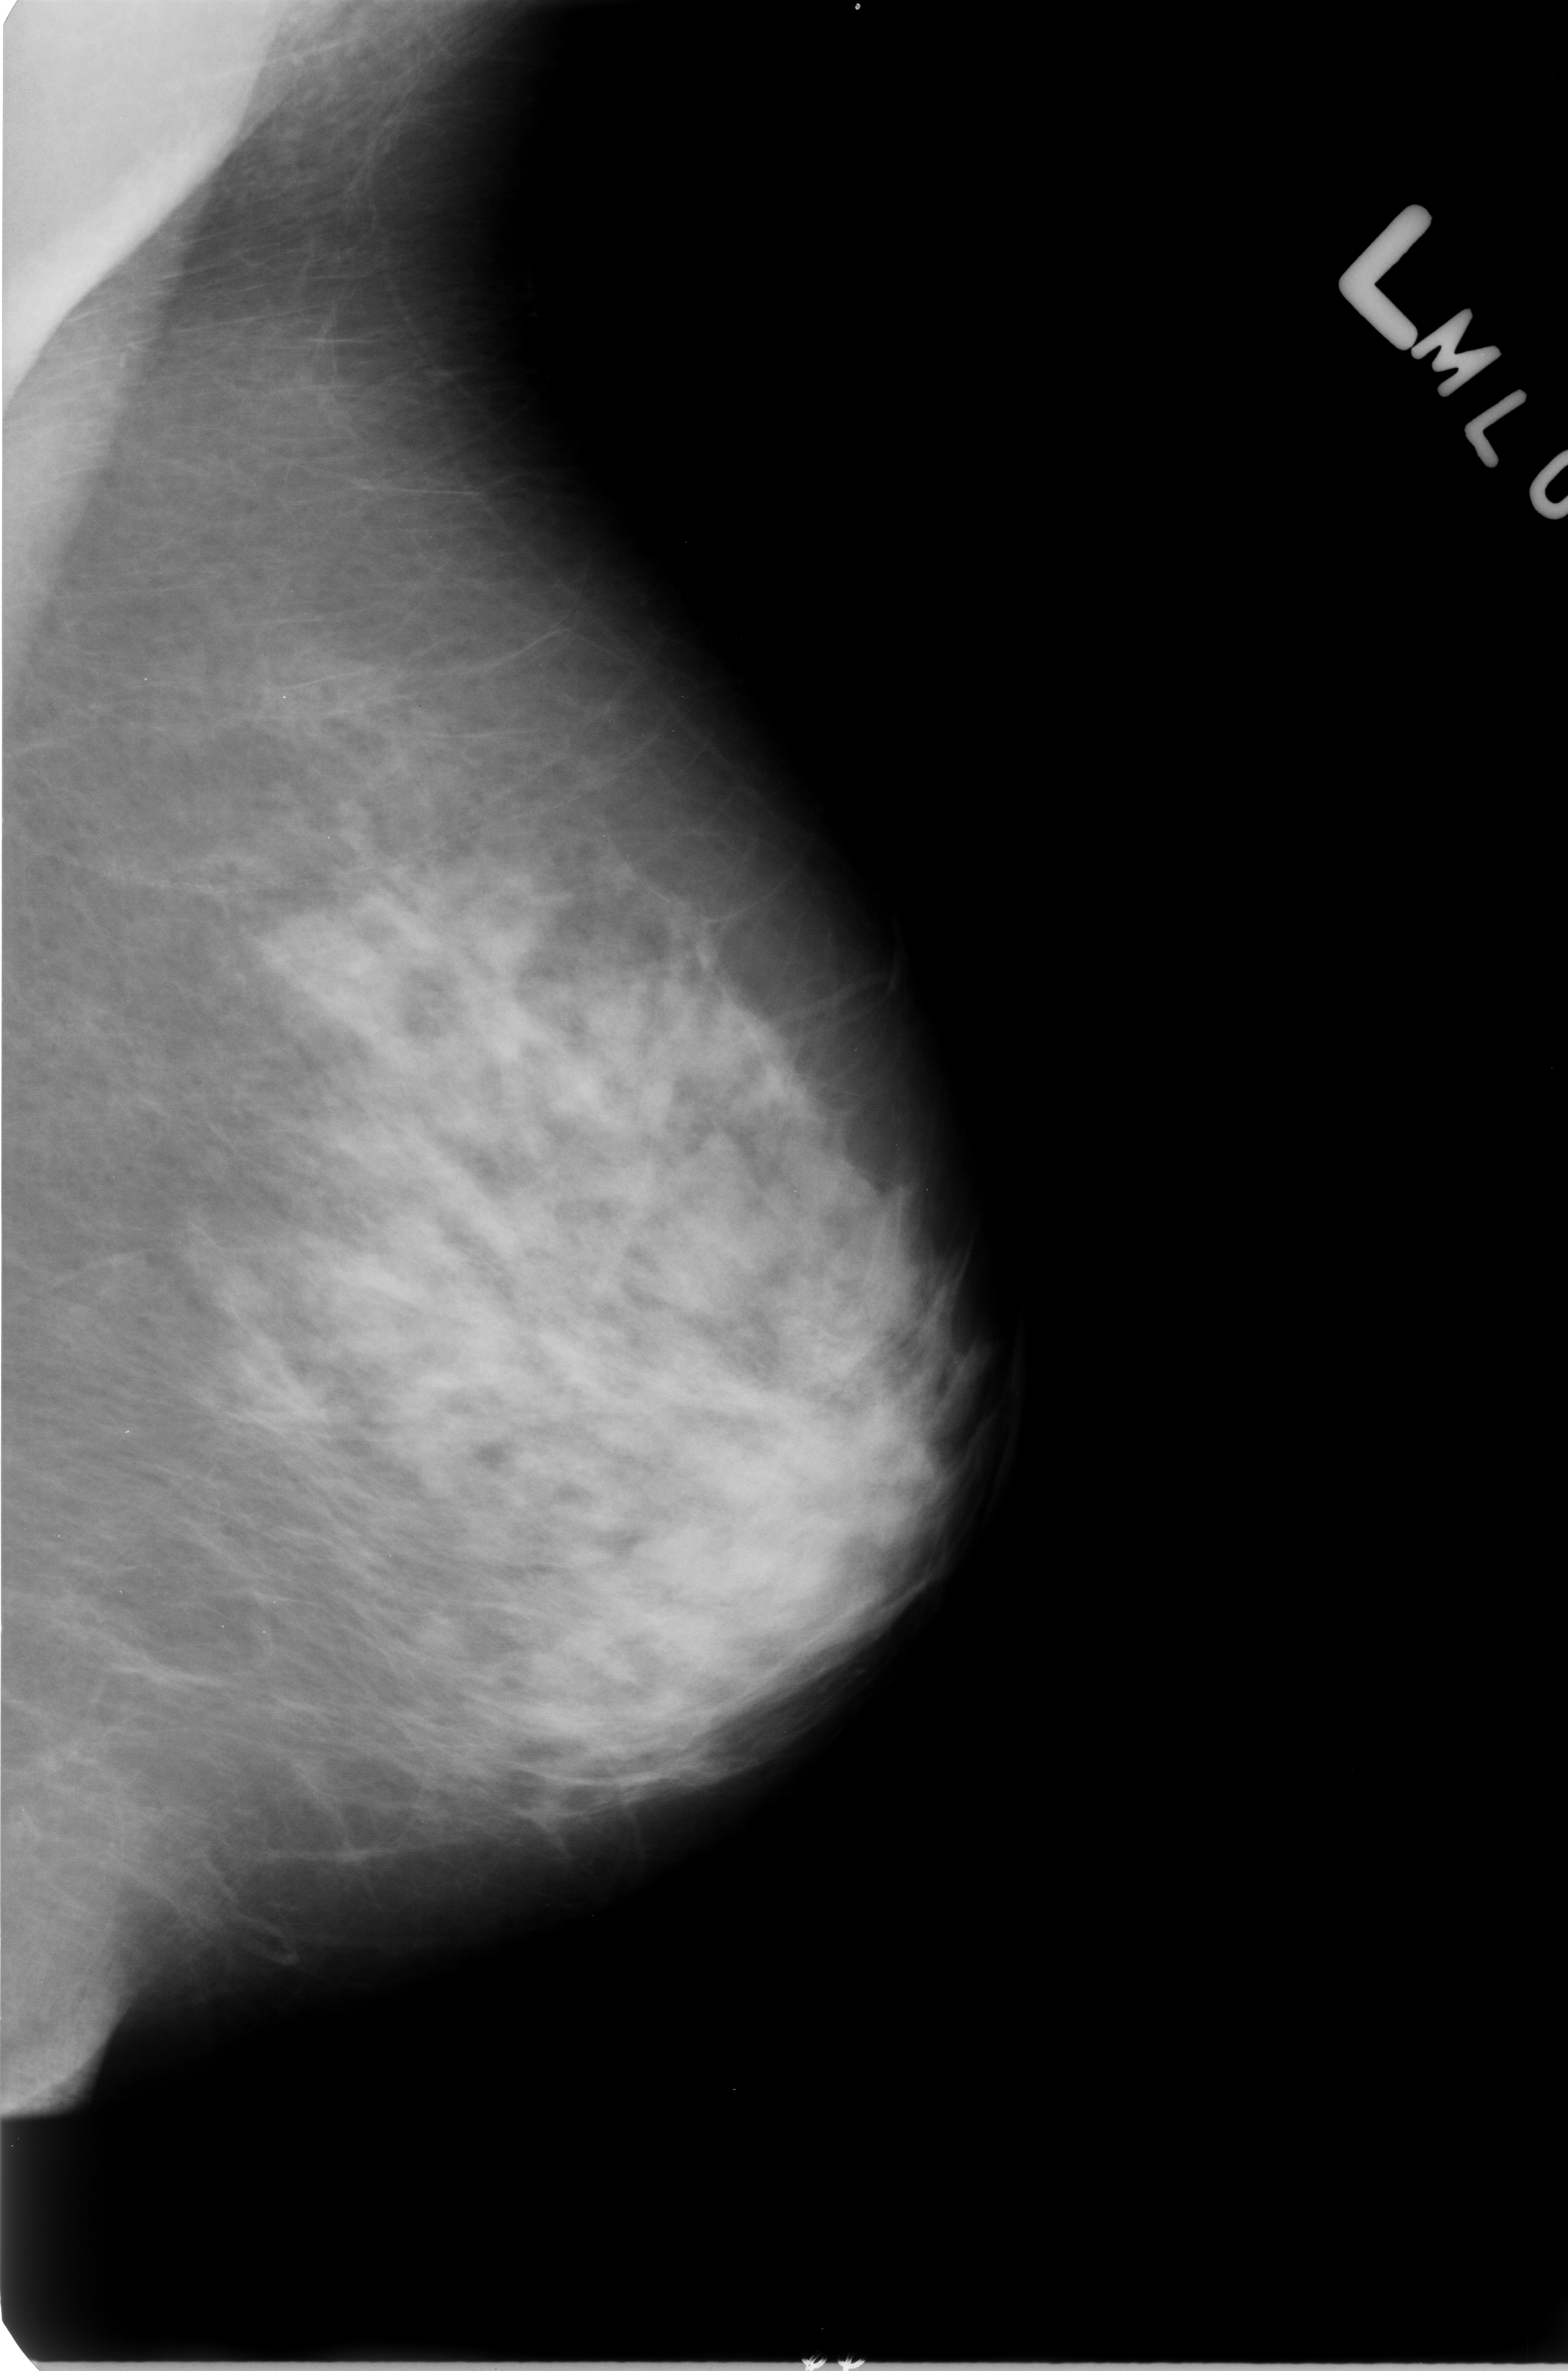
Digitized screen-film mammogram, left breast, MLO view, breast composition: heterogeneously dense (BI-RADS density category 3 of 4).
Marked abnormality: calcifications, morphology vascular; BI-RADS assessment category 2; benign without callback (not worked up further).